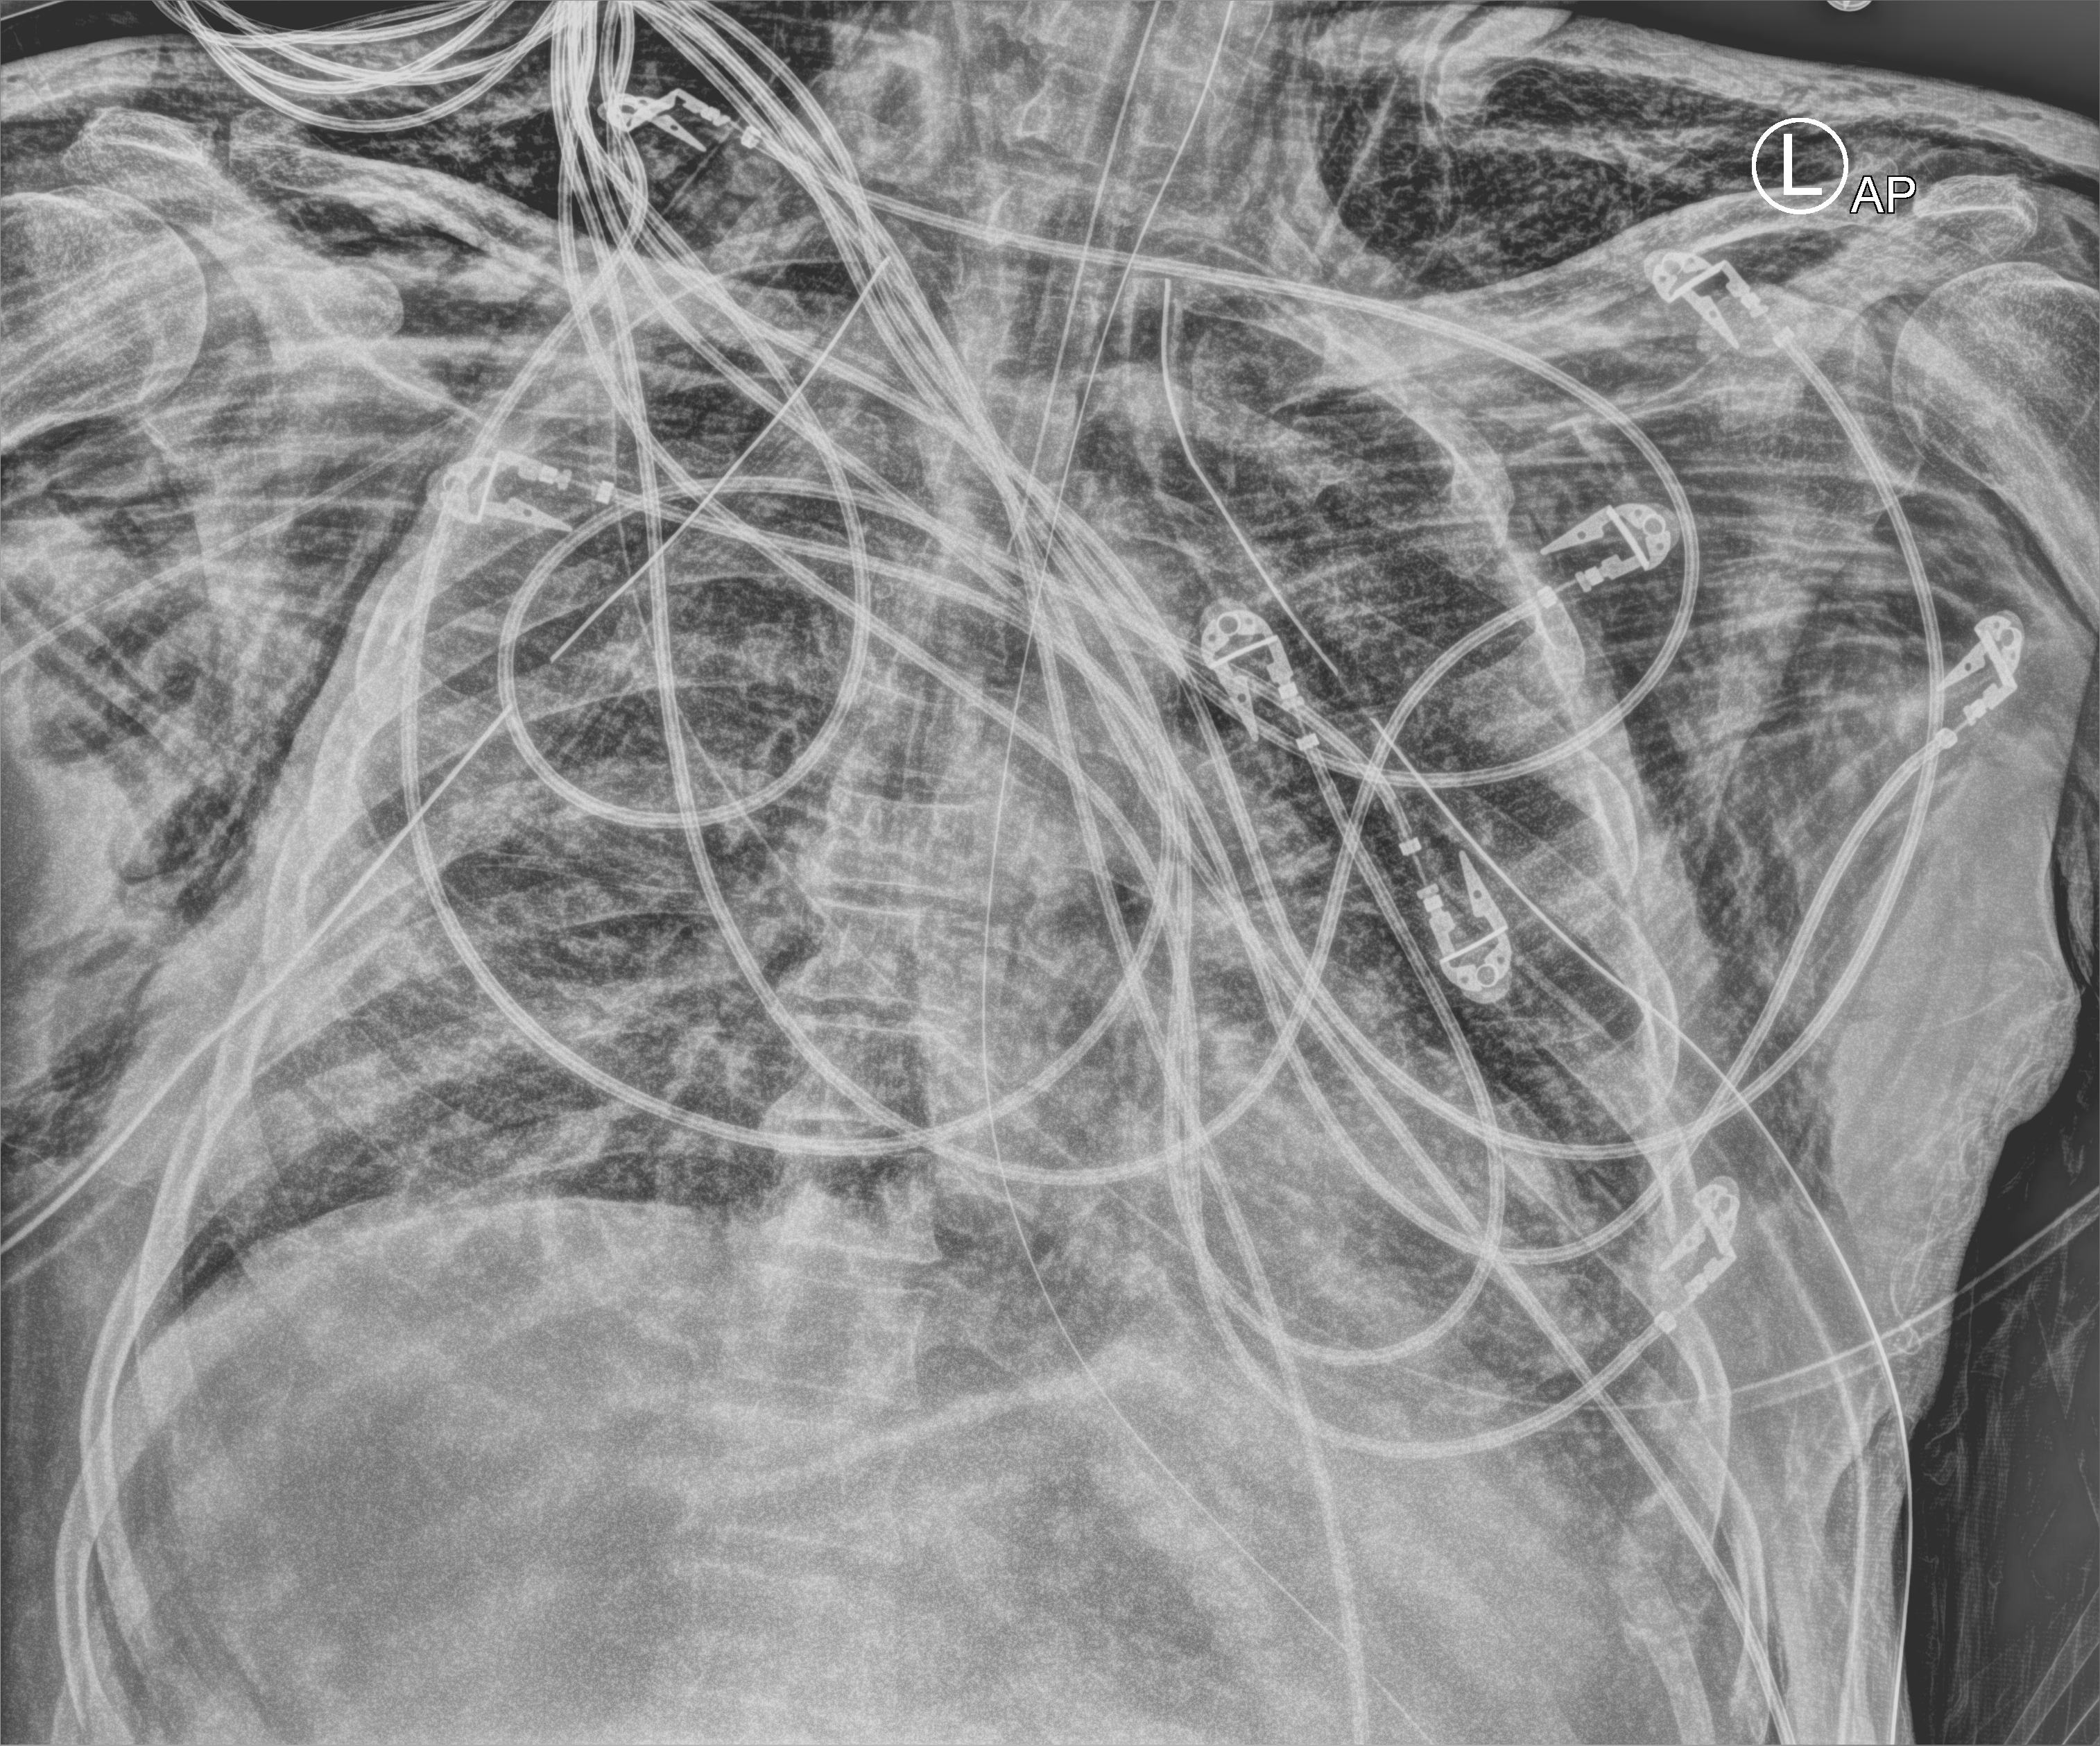
Chest X-ray (portable), anteroposterior (AP) projection. Patient hospitalised with COVID-19; male, aged 18–59 years.
Admission-level facts for this patient (not findings on this image; timing relative to this image not recorded):
- admitted to intensive care during this hospital stay: yes